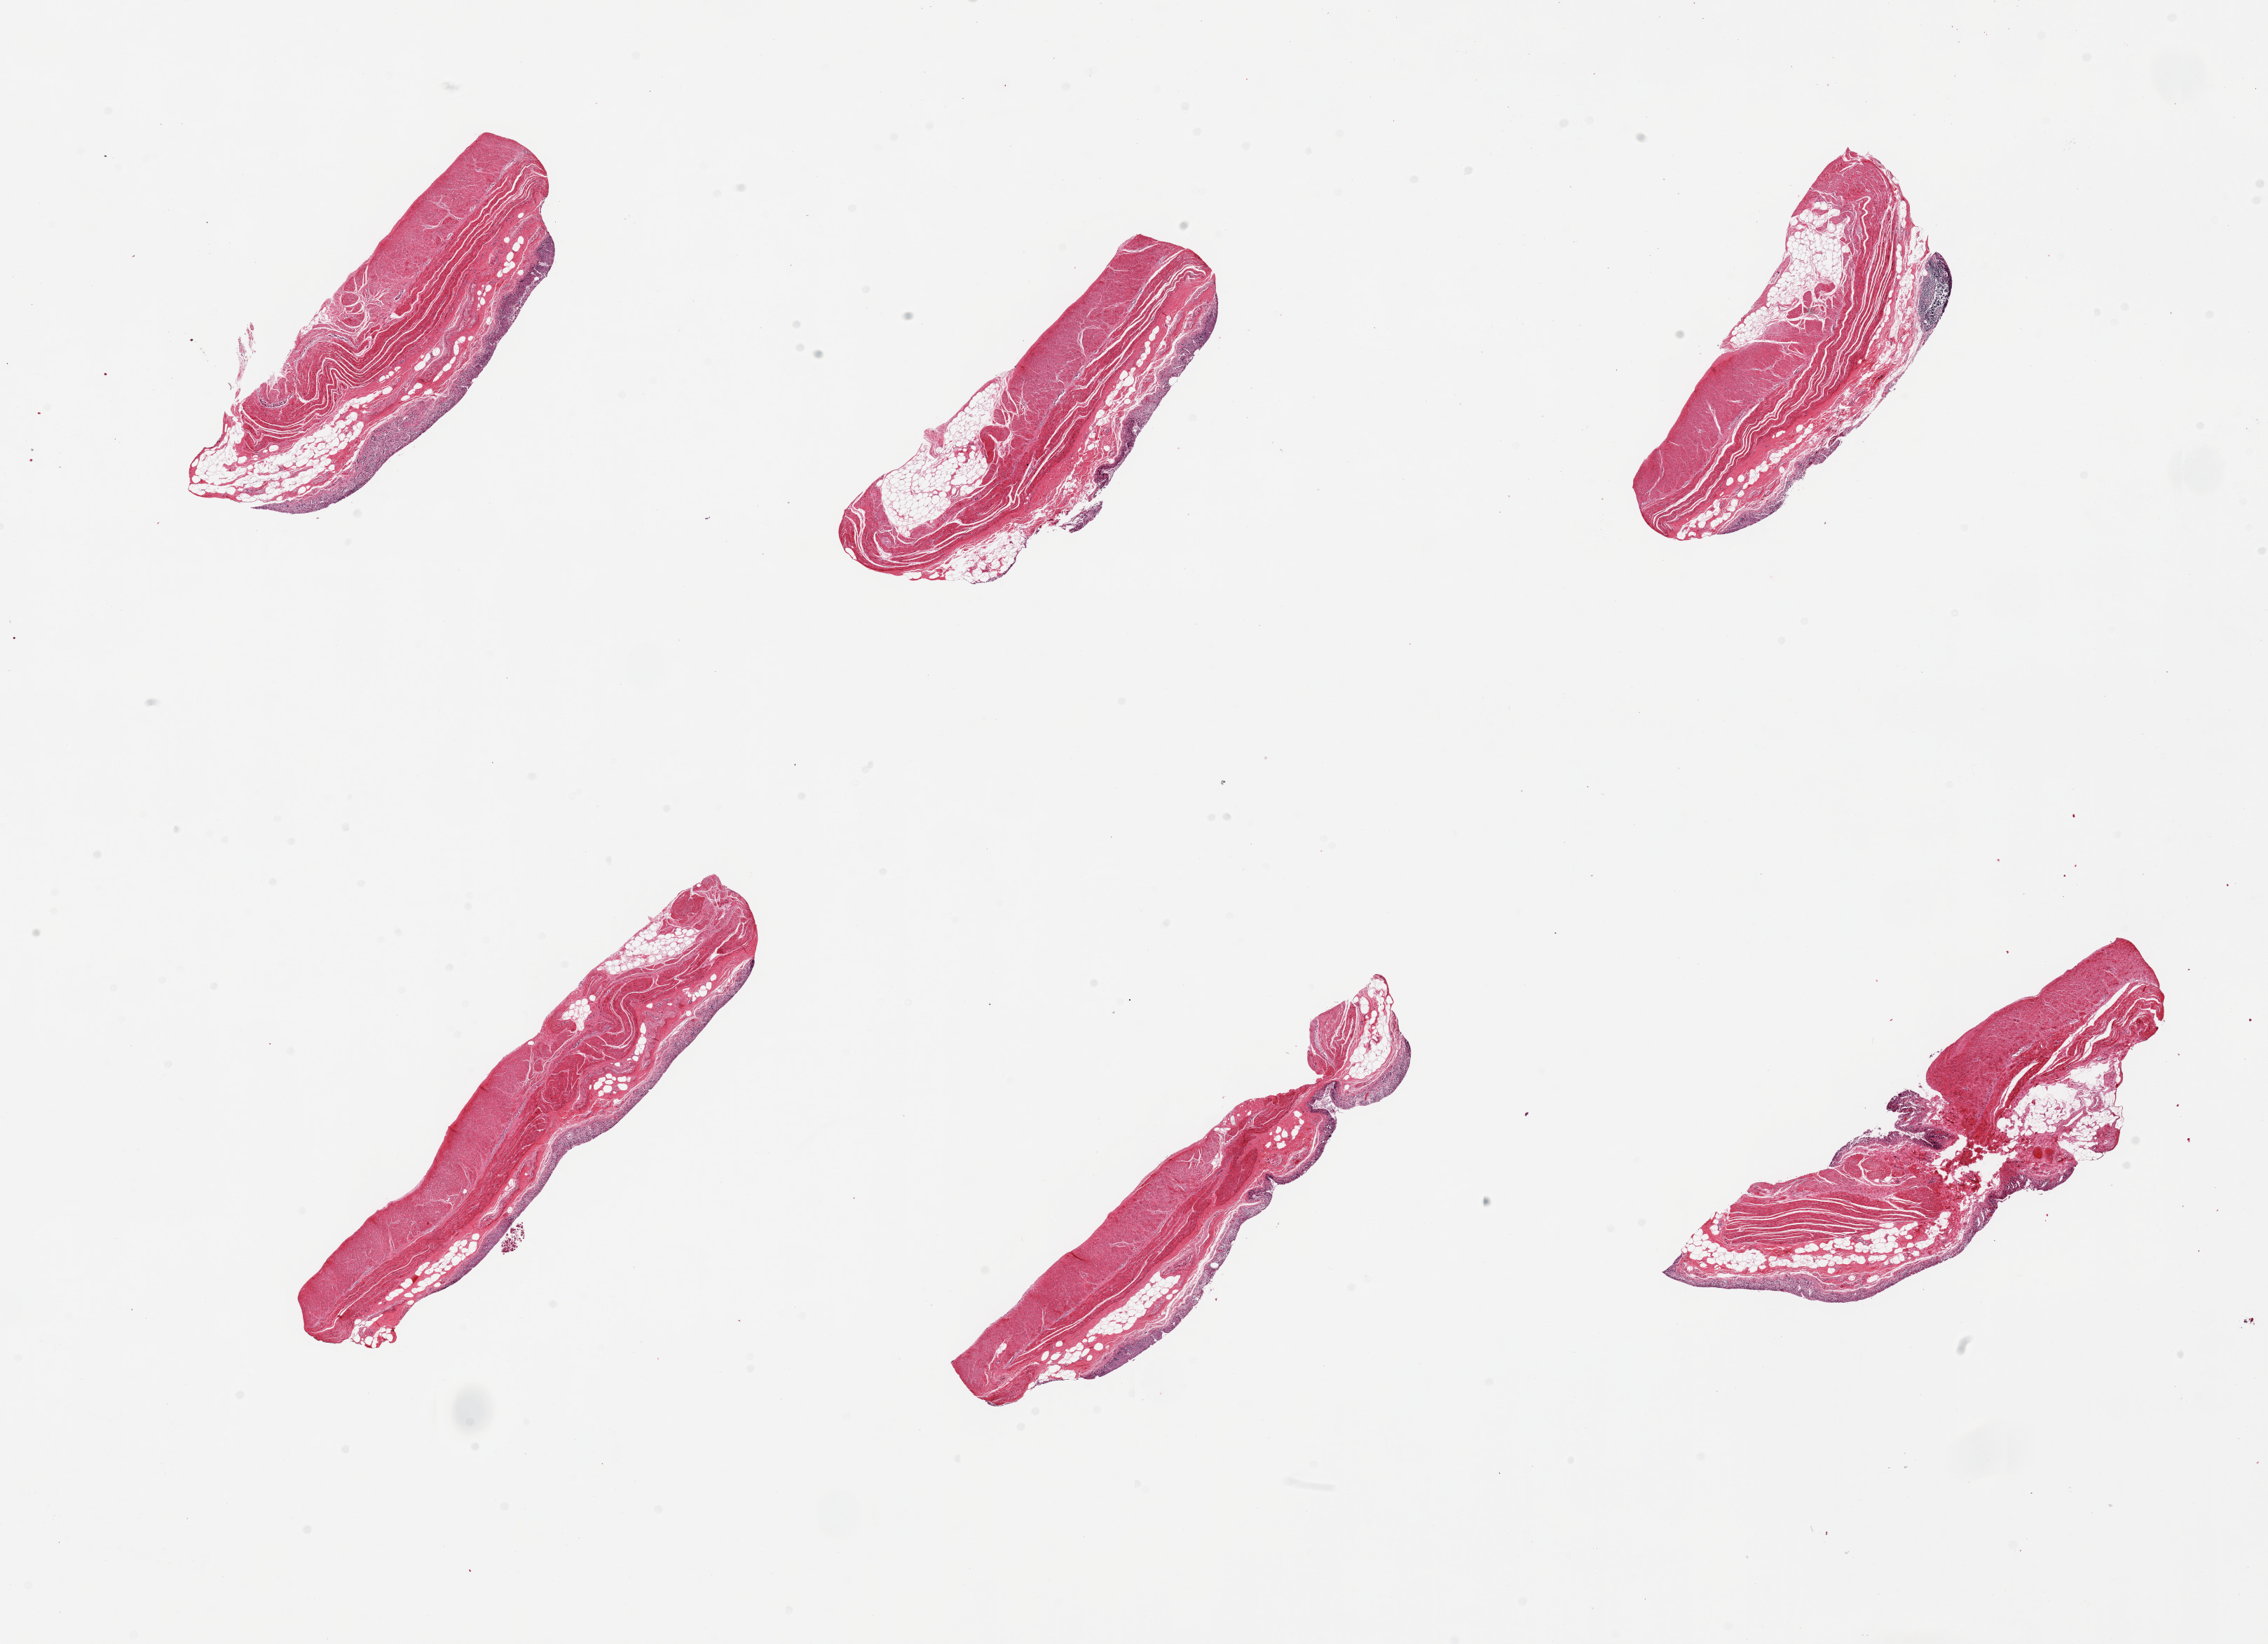
H&E whole-slide image — low-resolution overview of the scanned area, about 25.6 x 18.6 mm (acquisition: 20x scan); PAXgene-fixed paraffin-embedded (PFPE) section; sampled site (target tissue): transverse colon; donor tissue sample. Female donor.
Reviewer comment on this tissue sample: 6 pieces; full thickness sections with autolyzed mucosa.